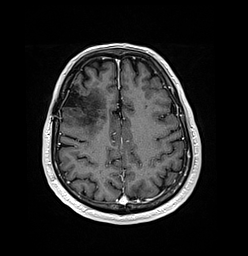
Brain MRI from a brain-tumour surgery series, one axial slice; slice 50 of 176 in the series (ordered by position); T1-weighted post-contrast; 1 mm slice thickness; 248 × 256 image matrix, field of view 242 × 250 mm. Case-level facts recorded for this patient, not image findings: histopathology: Oligodendroglioma; WHO grade: 3; IDH mutation: yes; tumour location: Right Frontal.
Outlined on this slice (outlined manually by an expert reader):
- previous resection cavity: bounding box (x1, y1, x2, y2) in pixels: (63, 88, 83, 108)